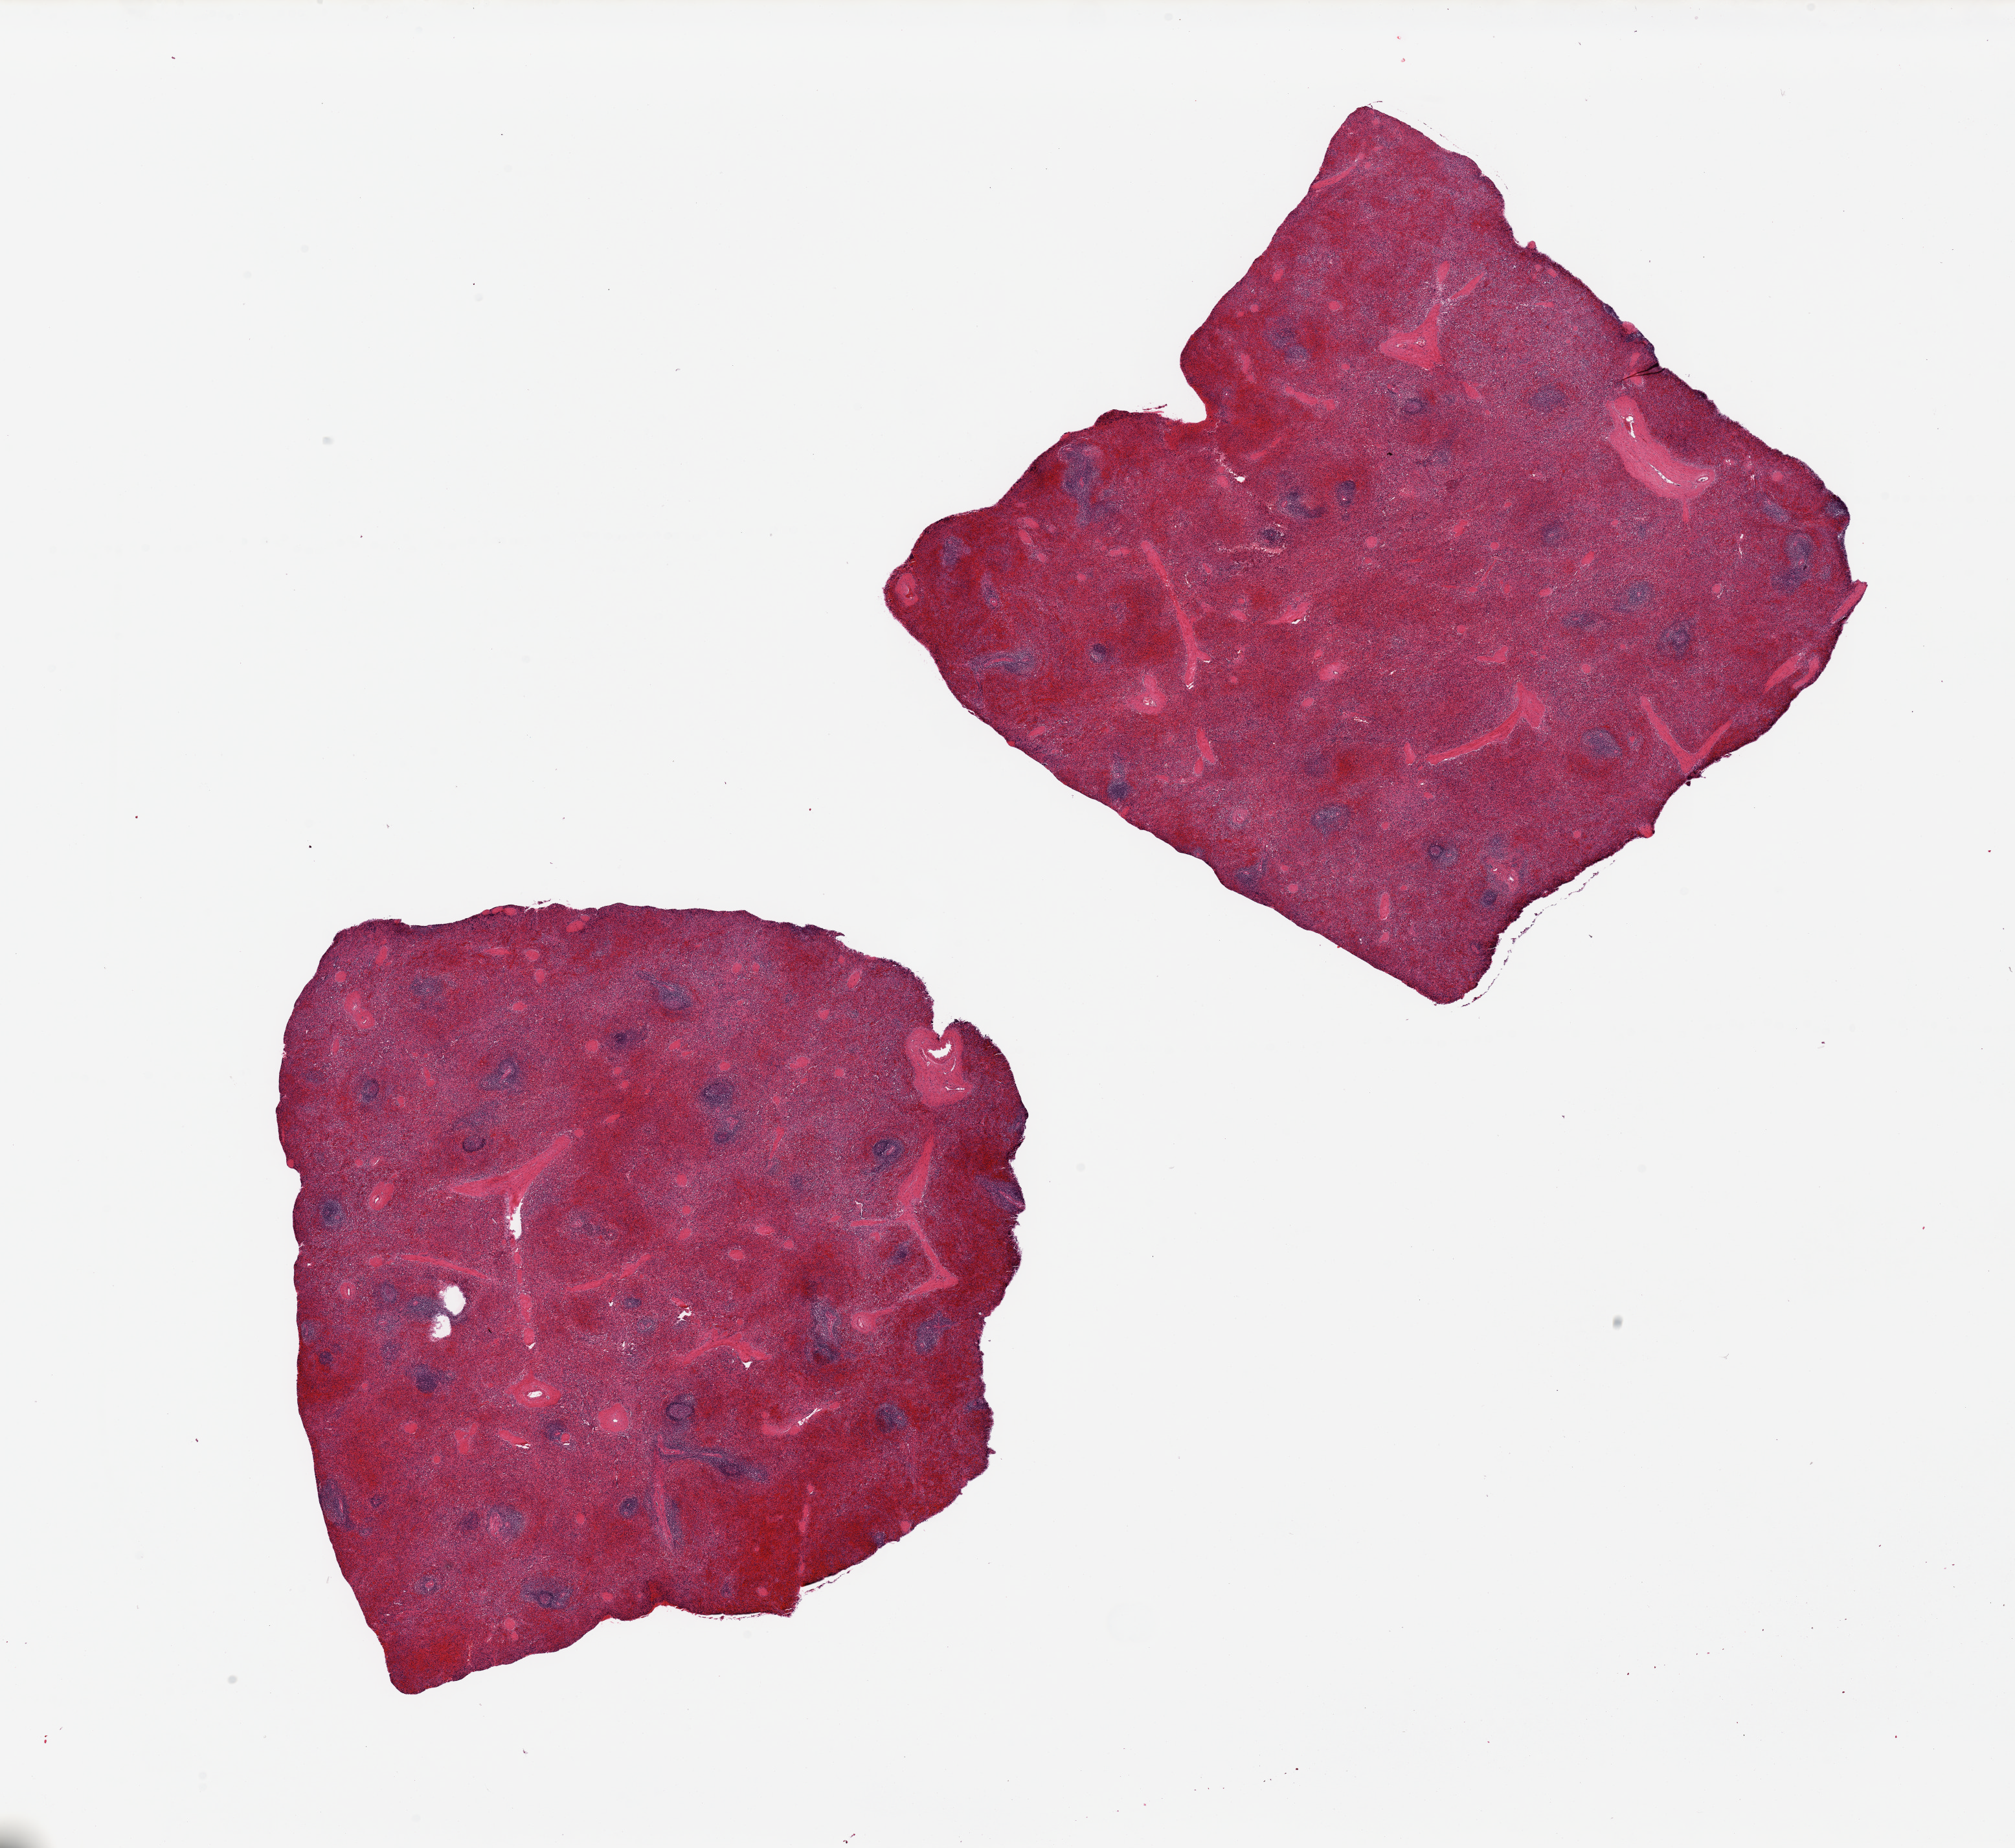
H&E whole-slide image — whole scanned area (about 24.6 x 22.6 mm) shown as a low-resolution overview, PAXgene-fixed paraffin-embedded (PFPE) section, sampled site (target tissue): spleen, tissue donor sample. Female donor.
Reviewer comment on this tissue sample: 2 pieces, marked congestion.